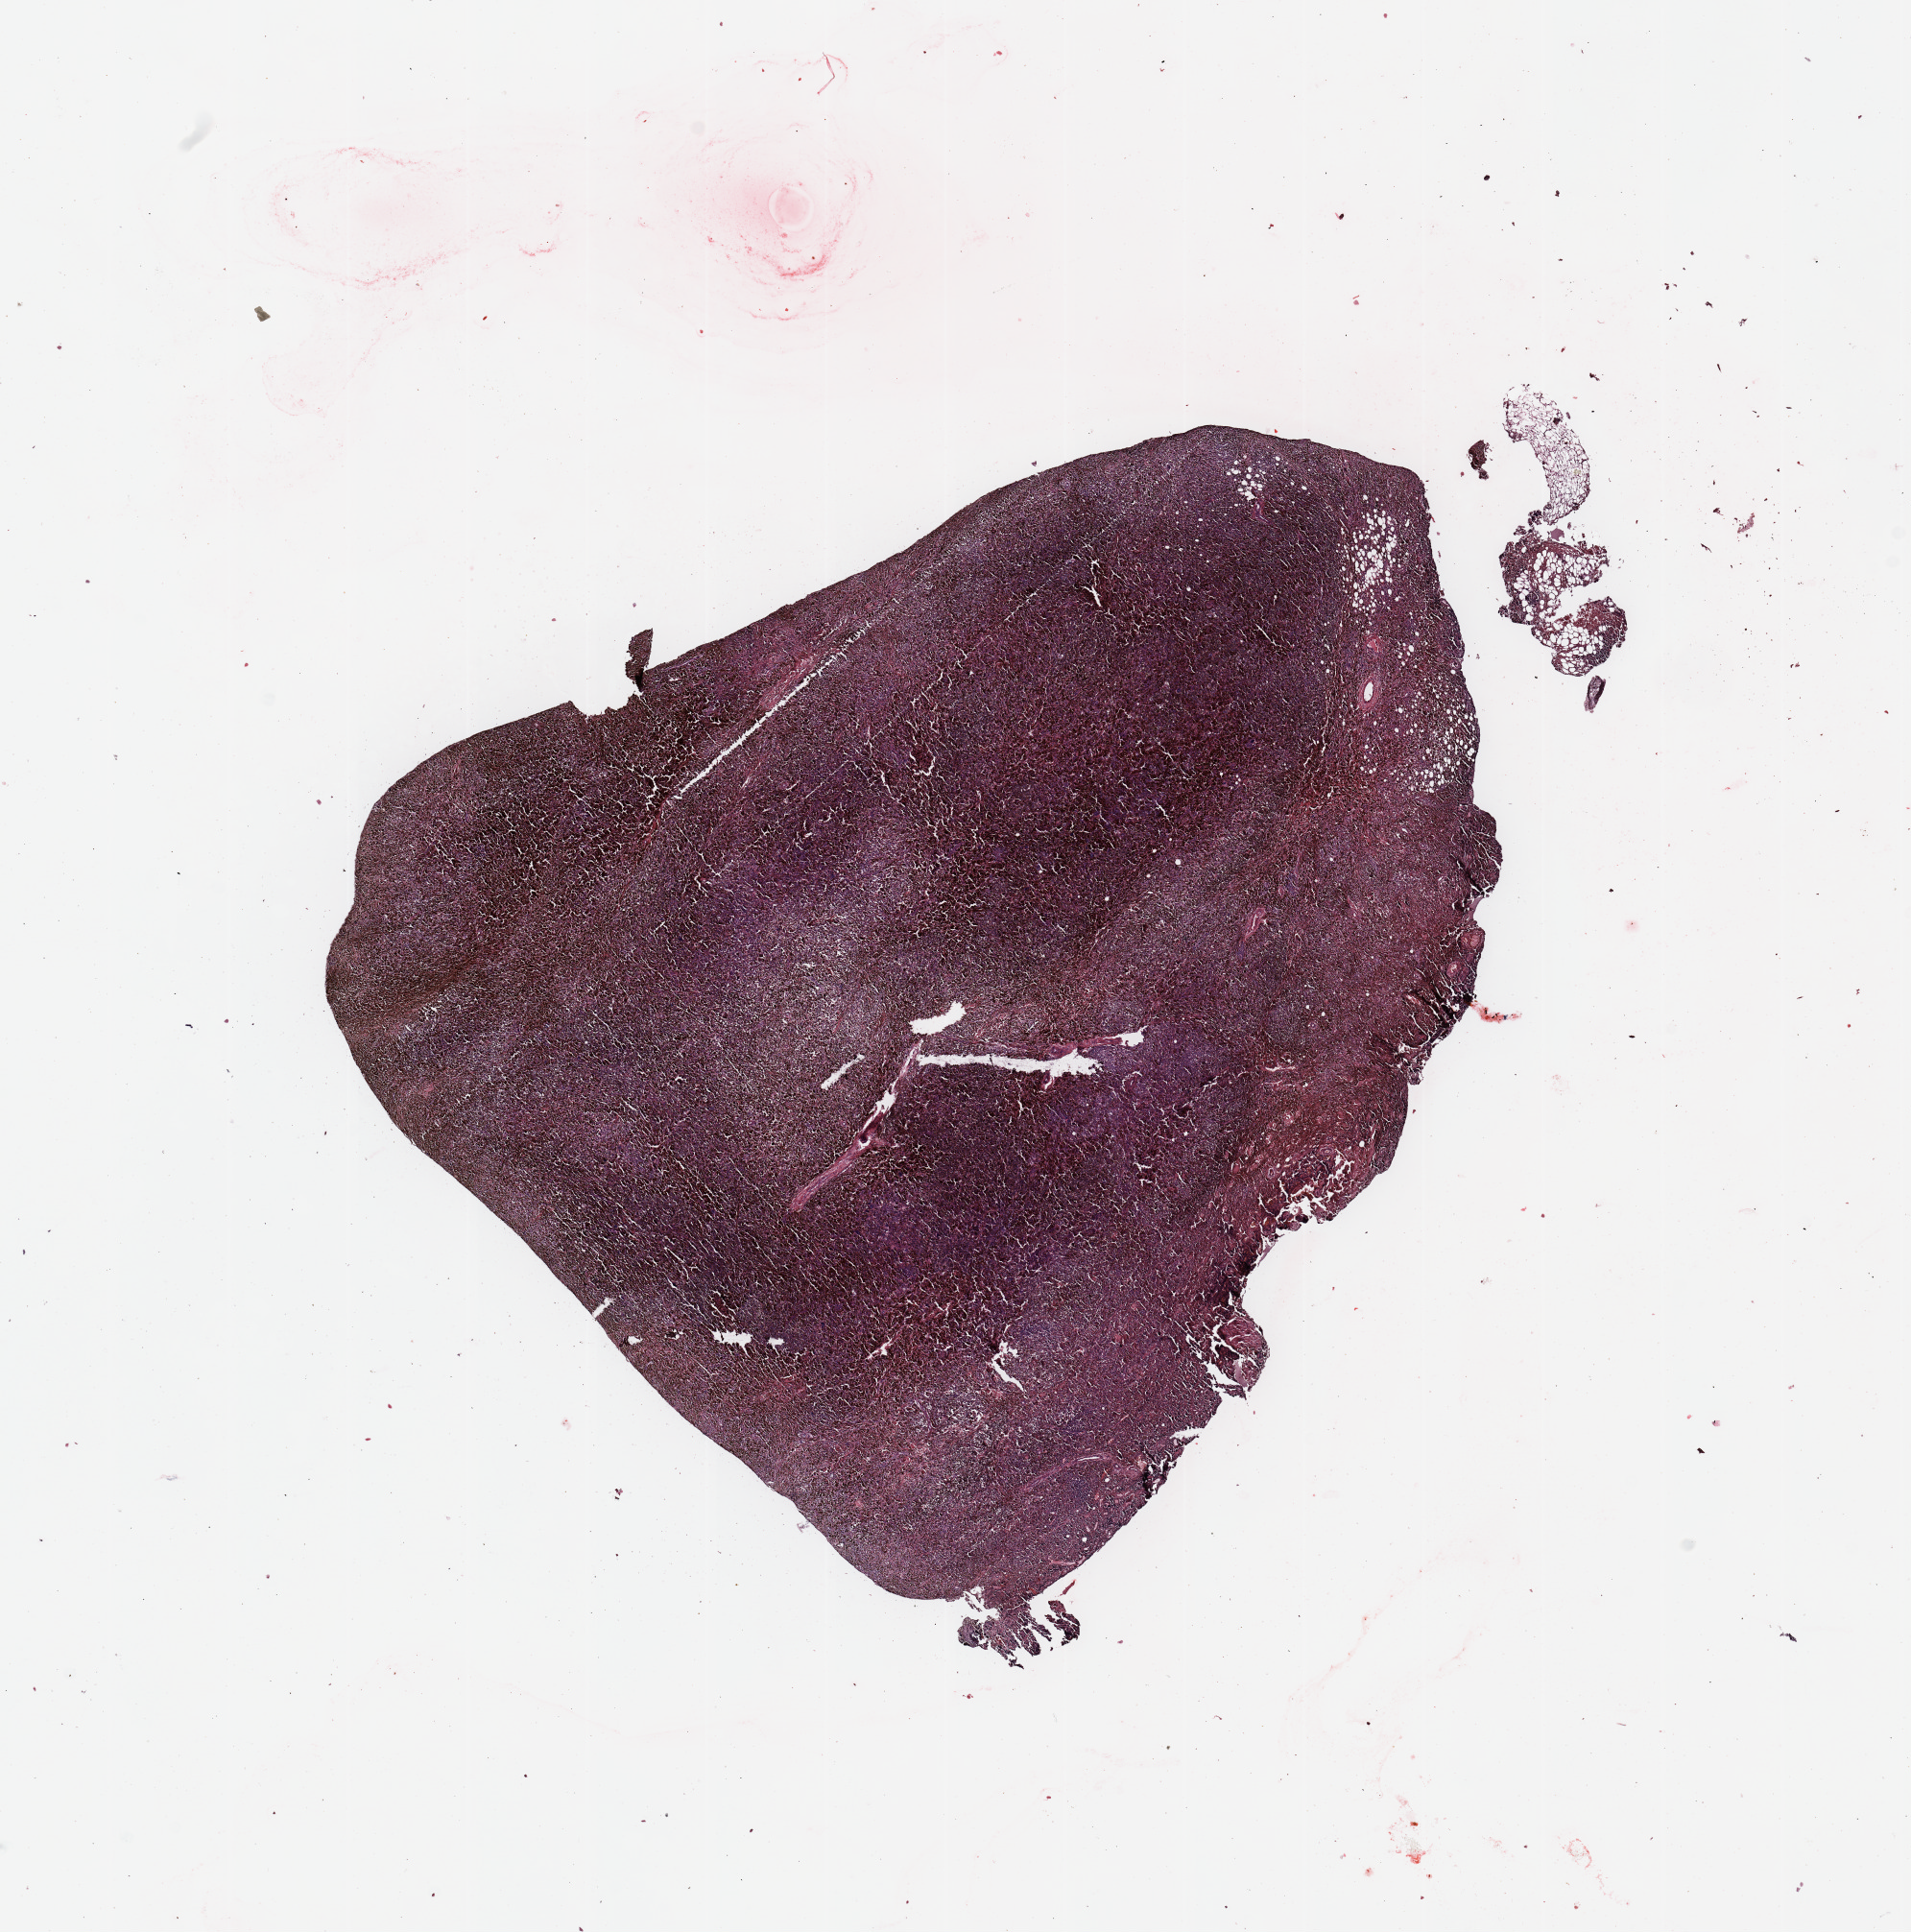
Whole-slide histology image, H&E, low-resolution overview of the scanned area, about 15.8 x 15.9 mm (from a 20x scan). Tumour tissue sample, sampled site: metastatic melanoma from an unknown primary site. 64-year-old male patient. Composition of this section per pathologist review: tumour nuclei 100%, necrosis 0%.
This section: metastatic tumour tissue. Patient diagnosis: Malignant melanoma, NOS.